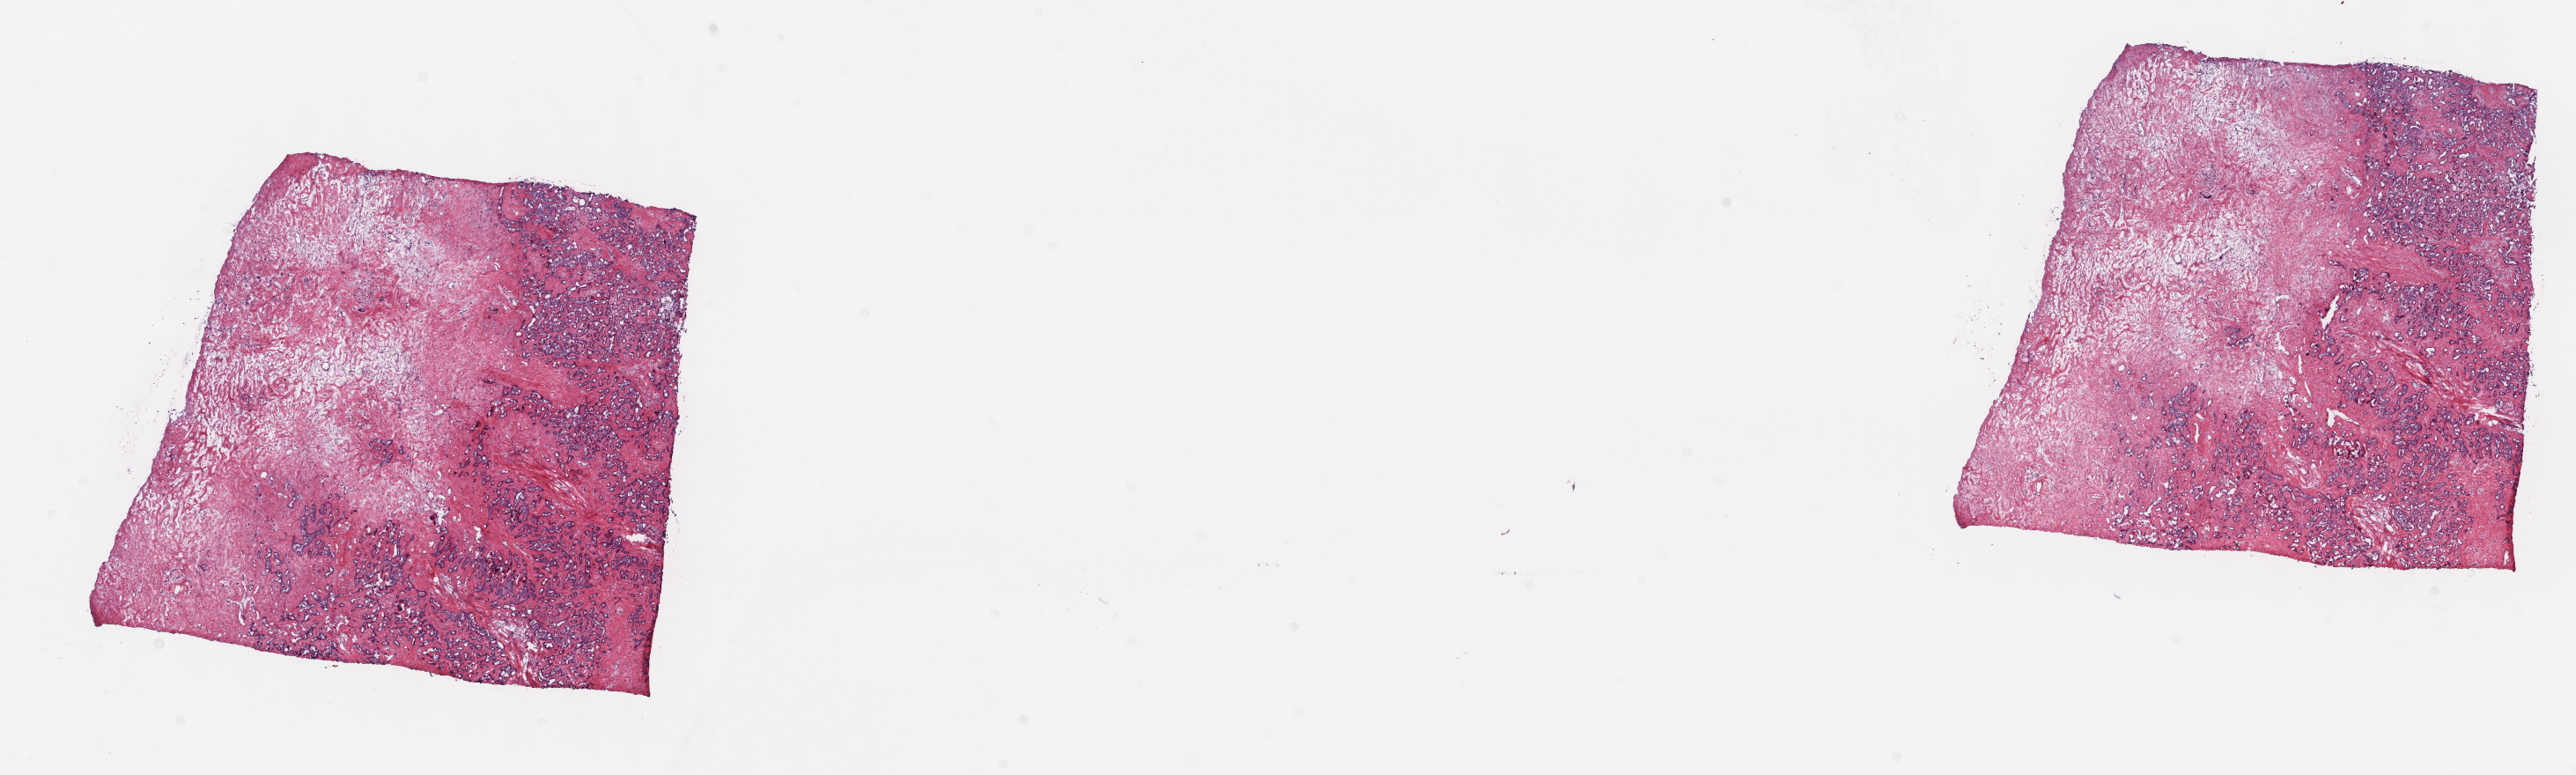
Digitized Hematoxylin and eosin (H&E) stained tissue section (whole slide), whole scanned area (about 23.7 x 7.1 mm, from a 40x scan) shown as a low-resolution overview, frozen section from the top of the tissue portion, primary tumour sample from the bile duct. Patient: male, age at initial diagnosis 68 years. Histologic grade: G2 (moderately differentiated). Composition of this section per pathologist review: tumour cells 65%, tumour nuclei 65%, normal cells 0%, stromal cells 33%, necrosis 2%. Inflammatory infiltration, as recorded: lymphocyte infiltration 3%, monocyte infiltration 2%, neutrophil infiltration 5%.
AJCC pathologic stage: II (6th edition). TNM: T2b N0 M0. Diagnosis: Cholangiocarcinoma (intrahepatic bile duct).